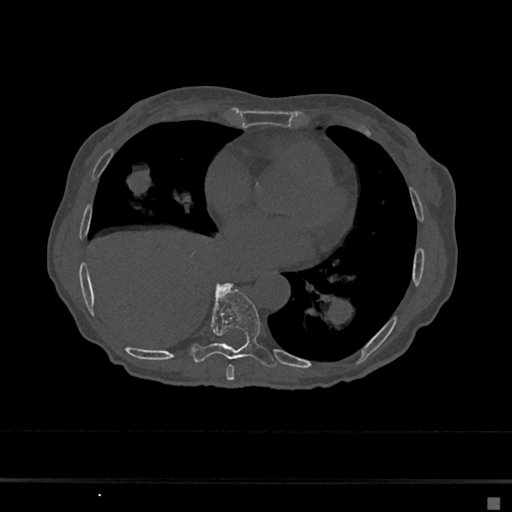
CT including the spine, one axial slice; slice 326 of 797 in the series (ordered by position); 120 kVp; bone window (W 1800 / L 400 HU); 512 × 512 image matrix, field of view 360 × 360 mm. Female patient, age 68 years. From the clinical record (not read from this slice): primary cancer: renal.
Annotated regions visible in this slice (semi-automatic segmentation, software-assisted and operator-edited):
- T7 vertebra: bounding box <226,365,235,381> (left, top, right, bottom; pixels)
- T8 vertebra: <191,283,277,368>